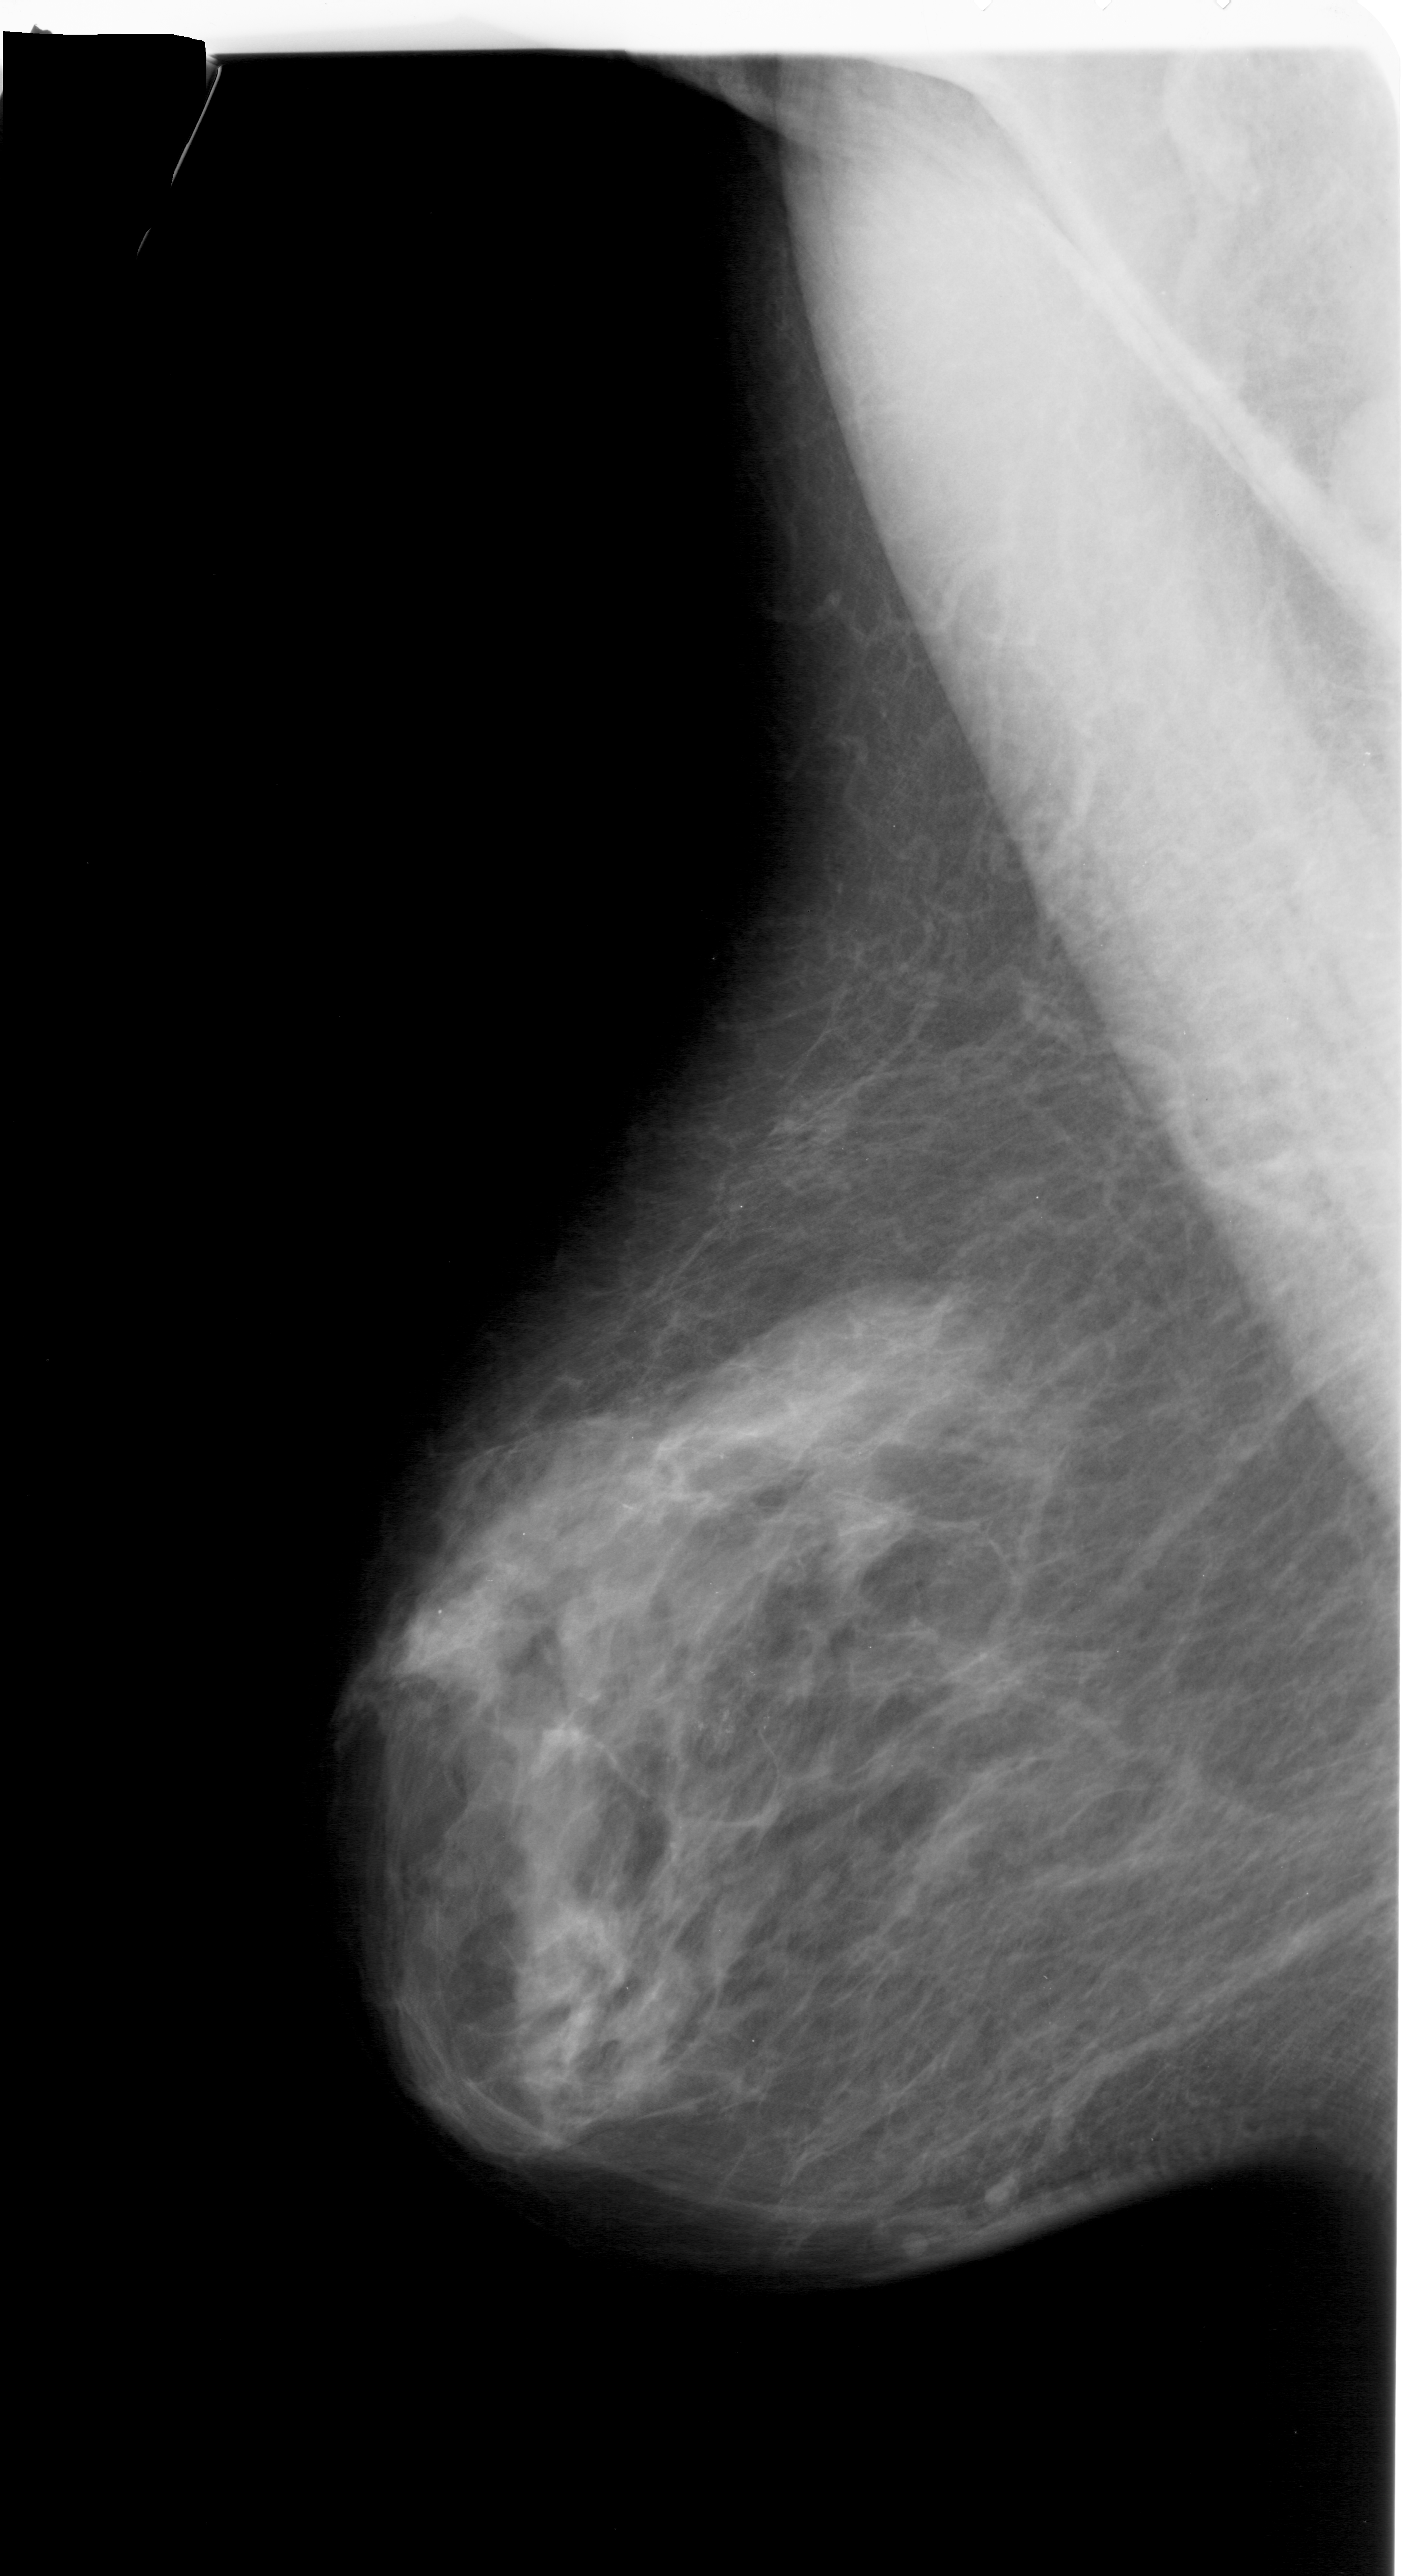
Mammogram (digitized film). Left breast. MLO view. BI-RADS breast density category 3 (scale 1–4). 1409 × 2576 image matrix.
Expert-marked regions of interest on this image (one box per marked abnormality):
- calcifications, morphology pleomorphic, distribution clustered; BI-RADS assessment category 4; pathology result (as recorded, not read from the image): benign: box from (x=596, y=1591) to (x=836, y=1837) px